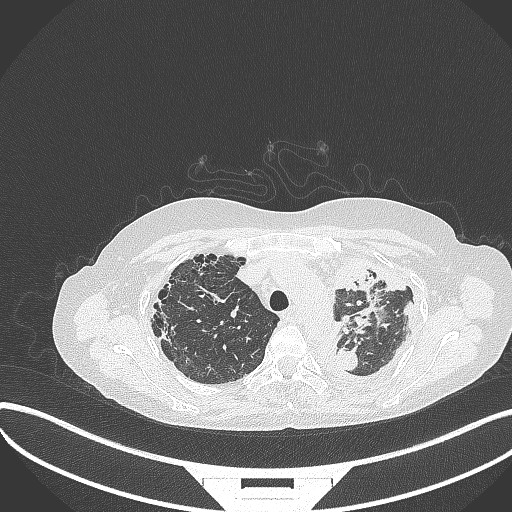
Chest CT, one axial slice. Position 263 of 373 along the scan axis. Reconstruction kernel B70f. Lung window (W 1500 / L -600 HU). 512 × 512 image matrix, field of view 400 × 400 mm. Female patient, age 56 years. From the clinical record (not read from this slice): clinical TNM (as recorded): T1 N0 M0.
Structures marked on this image (bounding box drawn by a radiologist):
- lung tumour (recorded histology: adenocarcinoma): bounding box [x1, y1, x2, y2] px = [337, 339, 365, 375]
- lung tumour (recorded histology: adenocarcinoma): [351, 255, 396, 328]